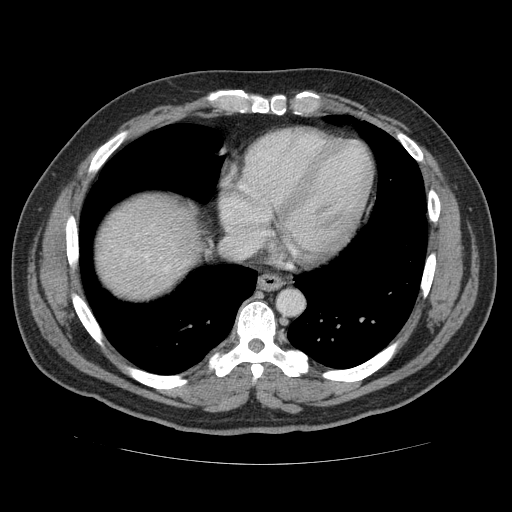
Contrast-enhanced abdominal CT (liver protocol), one axial slice; slice 109 of 113 in the series (ordered by position); reconstruction kernel STANDARD; 120 kVp; soft-tissue window (W 400 / L 40 HU); 512 × 512 image matrix, field of view 400 × 400 mm. From the clinical record (not read from this slice): diagnosis: hepatocellular carcinoma (patient treated with transarterial chemoembolisation; whether this scan precedes or follows treatment is not stated here); TNM stage (as recorded): Stage-II; Child-Pugh class: B; tumour differentiation: moderately differentiated.
Structures marked on this image (semi-automatically segmented with operator editing):
- abdominal aorta: box from (x=279, y=290) to (x=303, y=315) px
- liver parenchyma outside the tumour (the mass and vessels are separate outlines, so this box may not span the whole liver): (x=100, y=197)–(x=194, y=291)